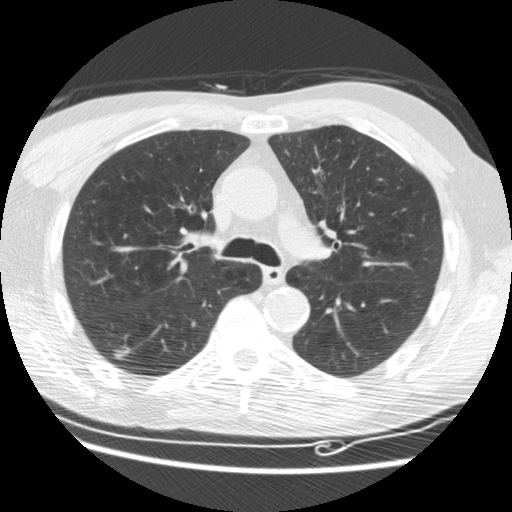
Low-dose screening chest CT, one axial slice; slice 113 of 176 in the series (ordered by position); lung window (W 1500 / L -600 HU); 512 × 512 image matrix, field of view 347 × 347 mm.
Structures marked on this image (outlined manually by an expert reader):
- lesion 1 (tumor, lower lobe of right lung): bounding box [x1, y1, x2, y2] px = [113, 346, 132, 360]